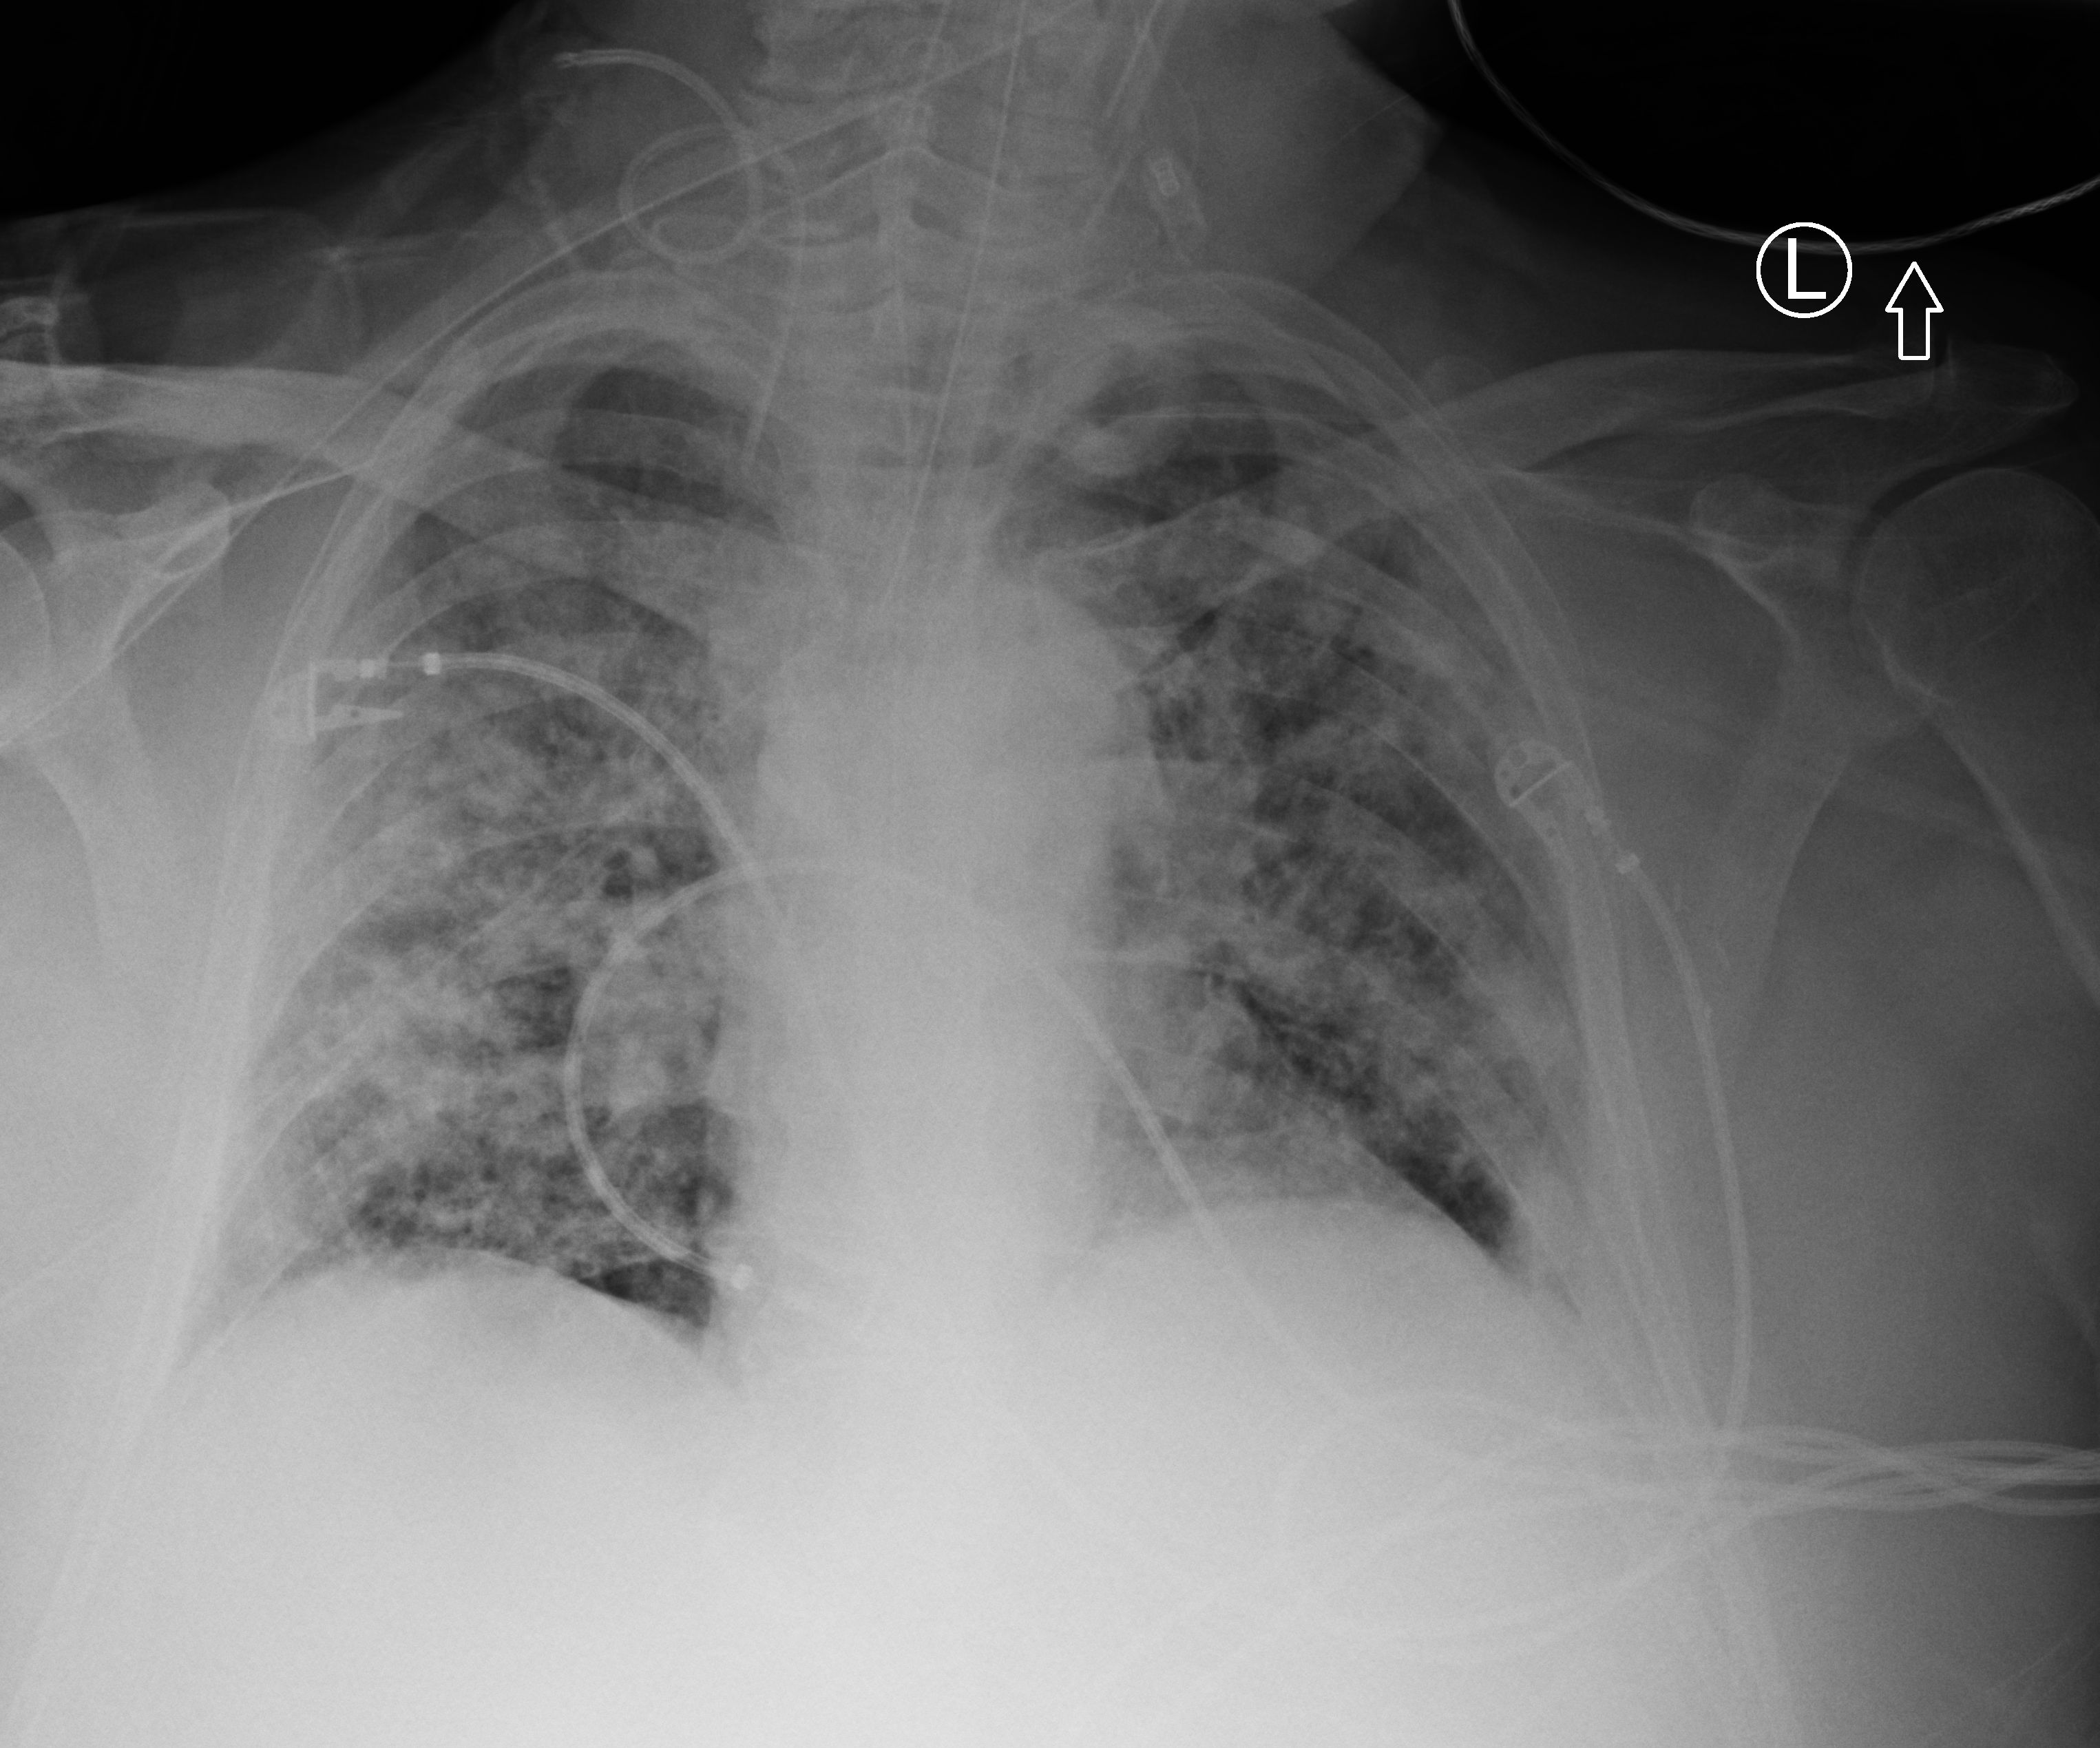
Portable chest radiograph, anteroposterior (AP) projection. Male patient hospitalised with COVID-19, age 60–74 years.
Hospital-stay facts (about this admission, not read from this image; timing relative to this image not recorded): hypertension (admission record): yes; admitted to intensive care during this hospital stay: yes.